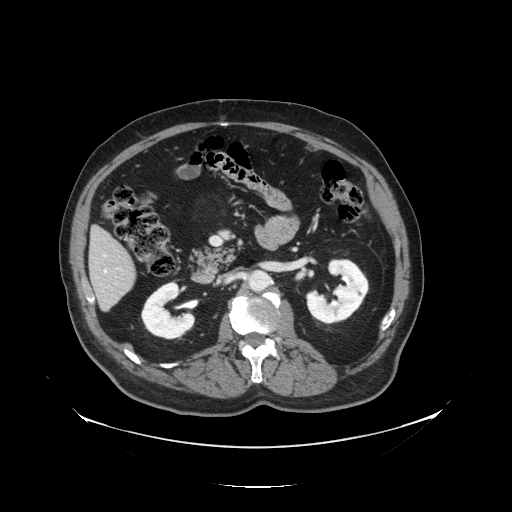
Contrast-enhanced abdominal CT, one axial slice. Position 52 of 138 along the scan axis. Reconstruction kernel STANDARD. 120 kVp. Soft-tissue window (W 400 / L 40 HU). 512 × 512 image matrix. Male patient, age 77 years. From the clinical record (not read from this slice): diagnosis: colorectal cancer liver metastases, imaged before liver resection; multiple liver metastases: no; largest metastasis: 1.5 cm; disease in both lobes: no.
Annotated regions visible in this slice (outlined manually by an expert reader):
- liver: bounding box <91,230,138,310> (left, top, right, bottom; pixels)
- planned liver remnant (the part of the liver to remain after resection): <91,230,135,281>